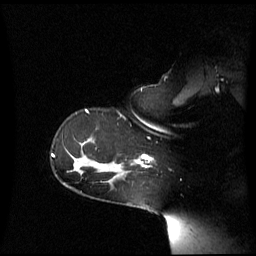
Breast MRI (dynamic contrast-enhanced), one sagittal slice; position 47 of 60 along the scan axis; dynamic contrast-enhanced series, image 2 of 3 at this slice position (ordered by acquisition); 1.5 T; TE 4.2 ms, TR 8.4 ms; 256 × 256 image matrix, field of view 270 × 270 mm. Female patient, age 39 years. Case-level facts recorded for this patient, not image findings: setting: breast cancer imaged before/during neoadjuvant chemotherapy; receptor status: triple-negative.
Annotated regions visible in this slice (semi-automatically segmented with operator editing):
- analysis volume of interest (the breast-tissue region the enhancement analysis was run in; not a lesion): bounding box (x1, y1, x2, y2) in pixels: (117, 154, 151, 176)
- tumour enhancement mask (voxels above the 70 % enhancement threshold inside the analysis volume of interest): (135, 154, 151, 167)